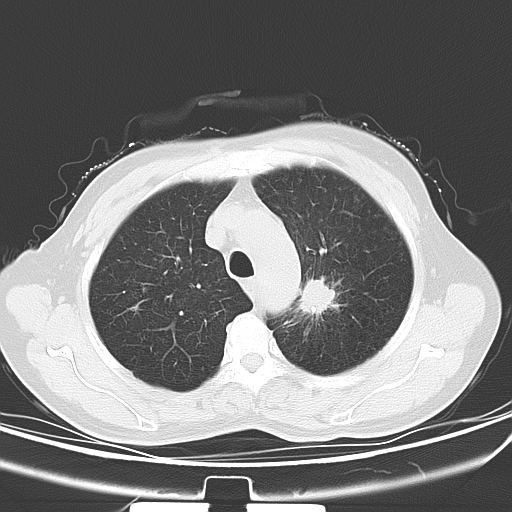
Chest CT, one axial slice. Position 44 of 53 along the scan axis. Lung window (W 1500 / L -600 HU). 512 × 512 image matrix. Female patient, age 60 years. Case-level facts recorded for this patient, not image findings: clinical TNM (as recorded): T1b N0 M0.
Outlined on this slice (rectangle marked by the reading radiologist):
- lung tumour (recorded histology: squamous cell carcinoma): bounding box [x1, y1, x2, y2] px = [295, 271, 344, 326]